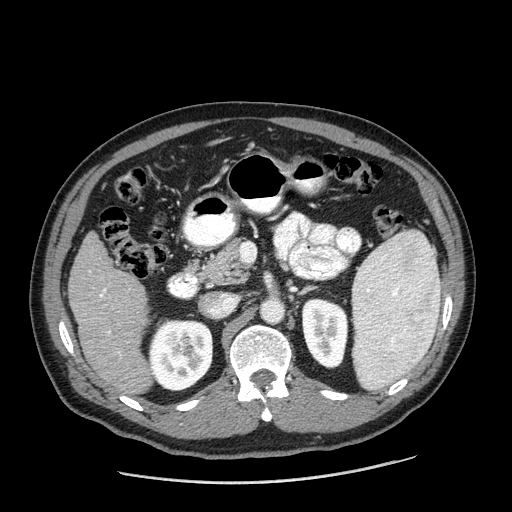
Contrast-enhanced abdominal CT (liver protocol), one axial slice. Position 81 of 198 along the scan axis. Reconstruction kernel STANDARD. 120 kVp. One of 2 acquisitions stored at this slice position. Soft-tissue window (W 400 / L 40 HU). 512 × 512 image matrix, field of view 400 × 400 mm. From the clinical record (not read from this slice): diagnosis: hepatocellular carcinoma (patient treated with transarterial chemoembolisation; whether this scan precedes or follows treatment is not stated here); TNM stage (as recorded): Stage-II; Child-Pugh class: A; tumour differentiation: moderately differentiated; tumour nodularity: multinodular.
Outlined on this slice (semi-automatically segmented with operator editing):
- liver parenchyma outside the tumour (the mass and vessels are separate outlines, so this box may not span the whole liver): bounding box <68,232,152,394> (left, top, right, bottom; pixels)
- liver vessels: <100,289,110,333>